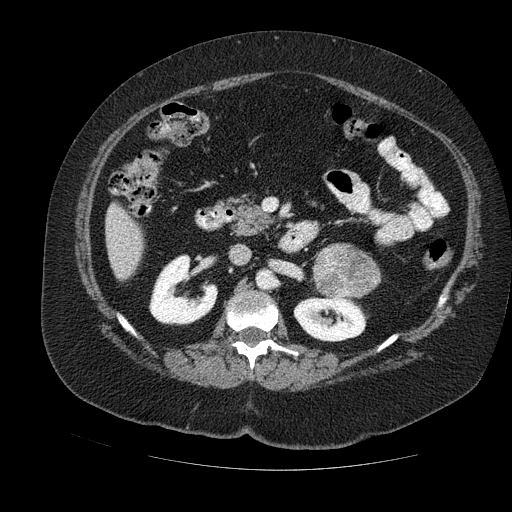
Contrast-enhanced abdominal CT, one axial slice. Position 58 of 121 along the scan axis. Soft-tissue window (W 400 / L 40 HU). 512 × 512 image matrix, field of view 420 × 420 mm. Female patient. From the clinical record (not read from this slice): diagnosis: adrenocortical carcinoma; tumour side: left adrenal; tumour size at pathology: 8 cm.
Annotated regions visible in this slice (semi-automatically segmented with operator editing):
- mass: bounding box [x1, y1, x2, y2] px = [316, 246, 380, 298]